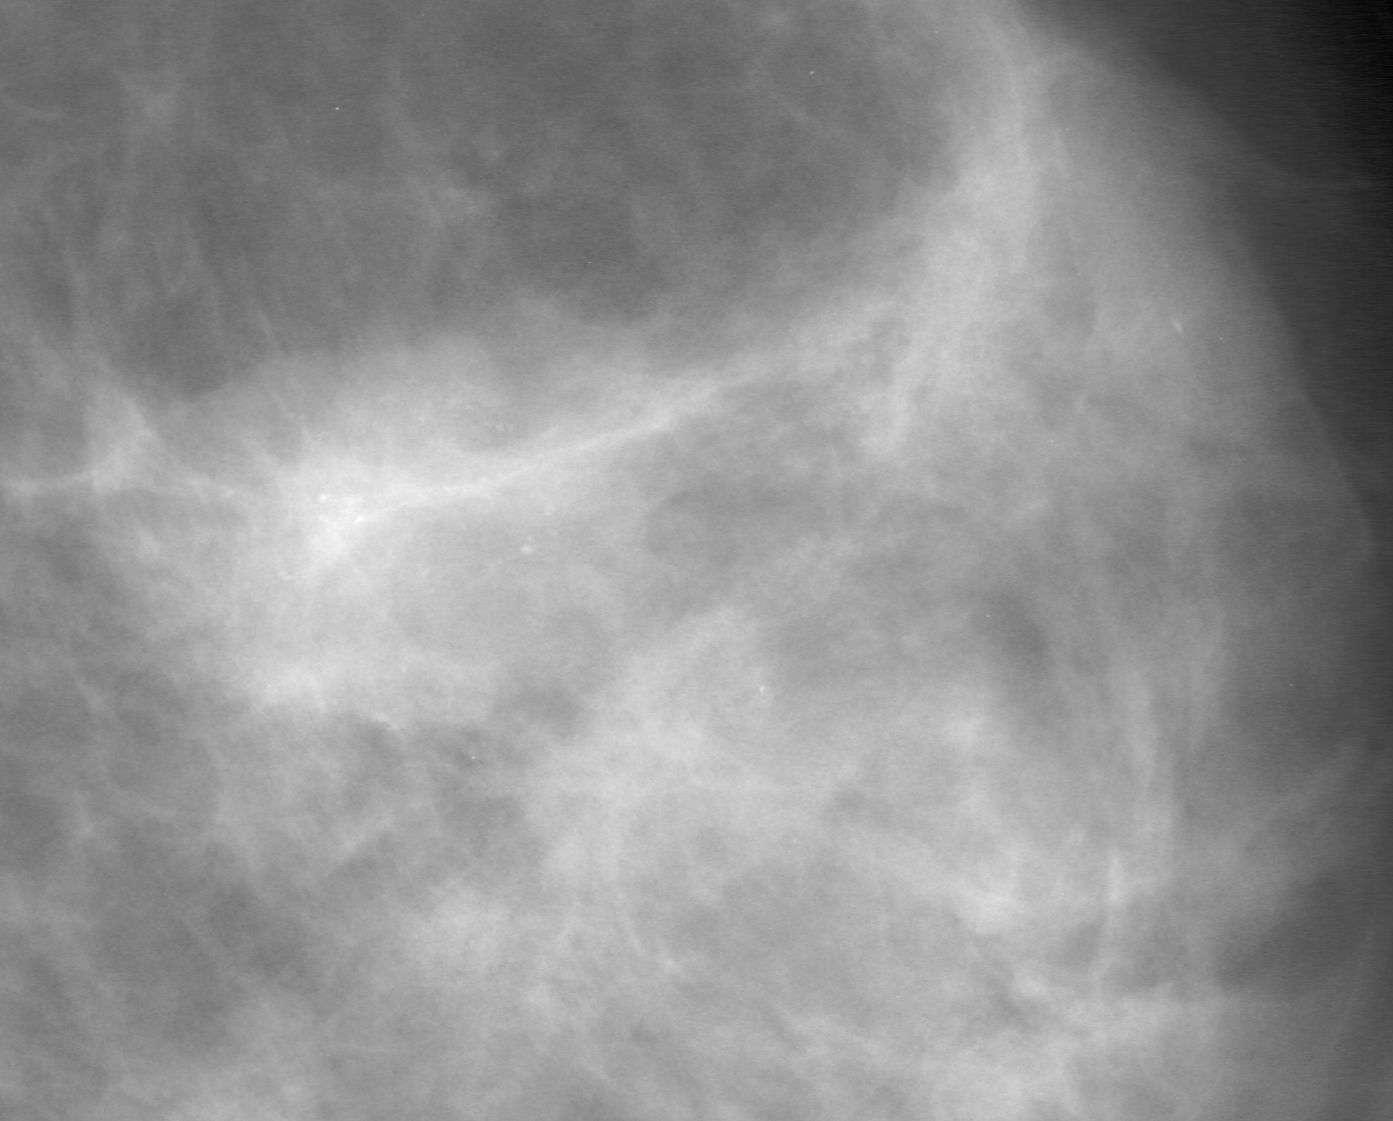
Cropped region of a digitized screen-film mammogram centred on a radiologist-marked abnormality; left breast; MLO view.
Finding: calcifications, morphology amorphous, distribution segmental; BI-RADS assessment category 4; subtlety rating 3 on a 1 (subtle) to 5 (obvious) scale; pathology result (as recorded, not read from the image): malignant.